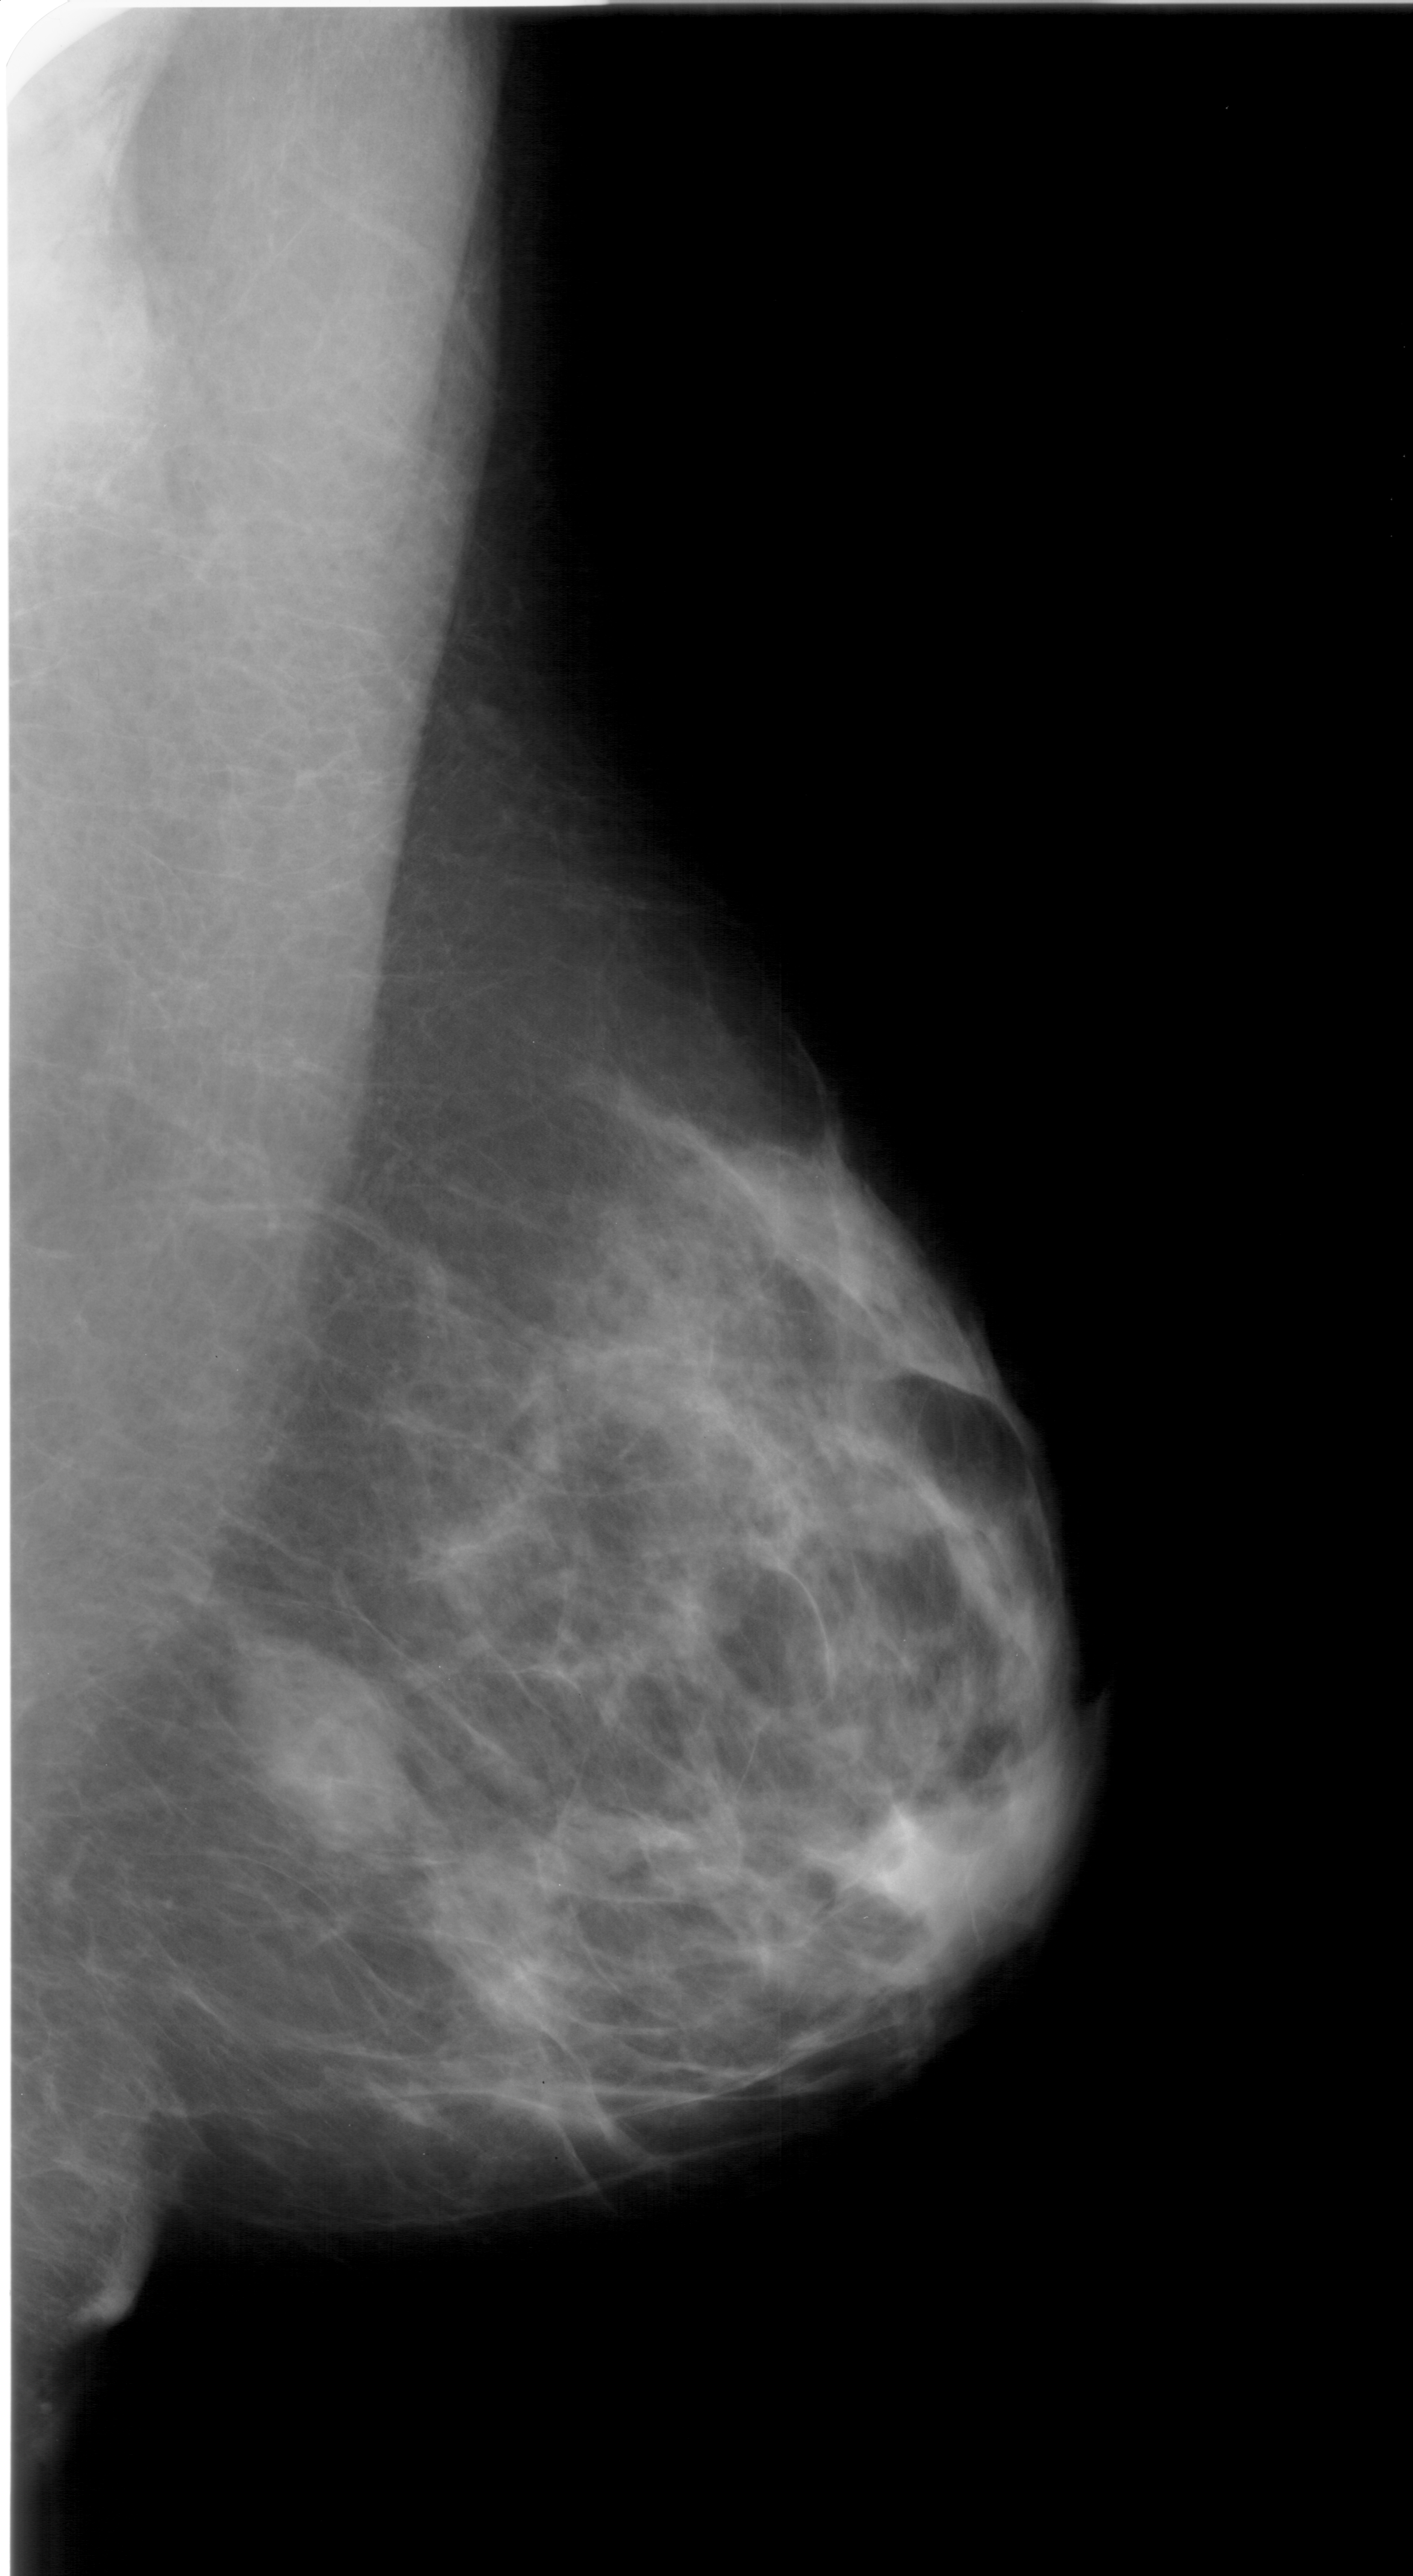
Mammogram (digitized film), right breast, MLO view.
Mass, shape oval, margins ill defined; BI-RADS assessment category 4; pathology (as recorded): benign.